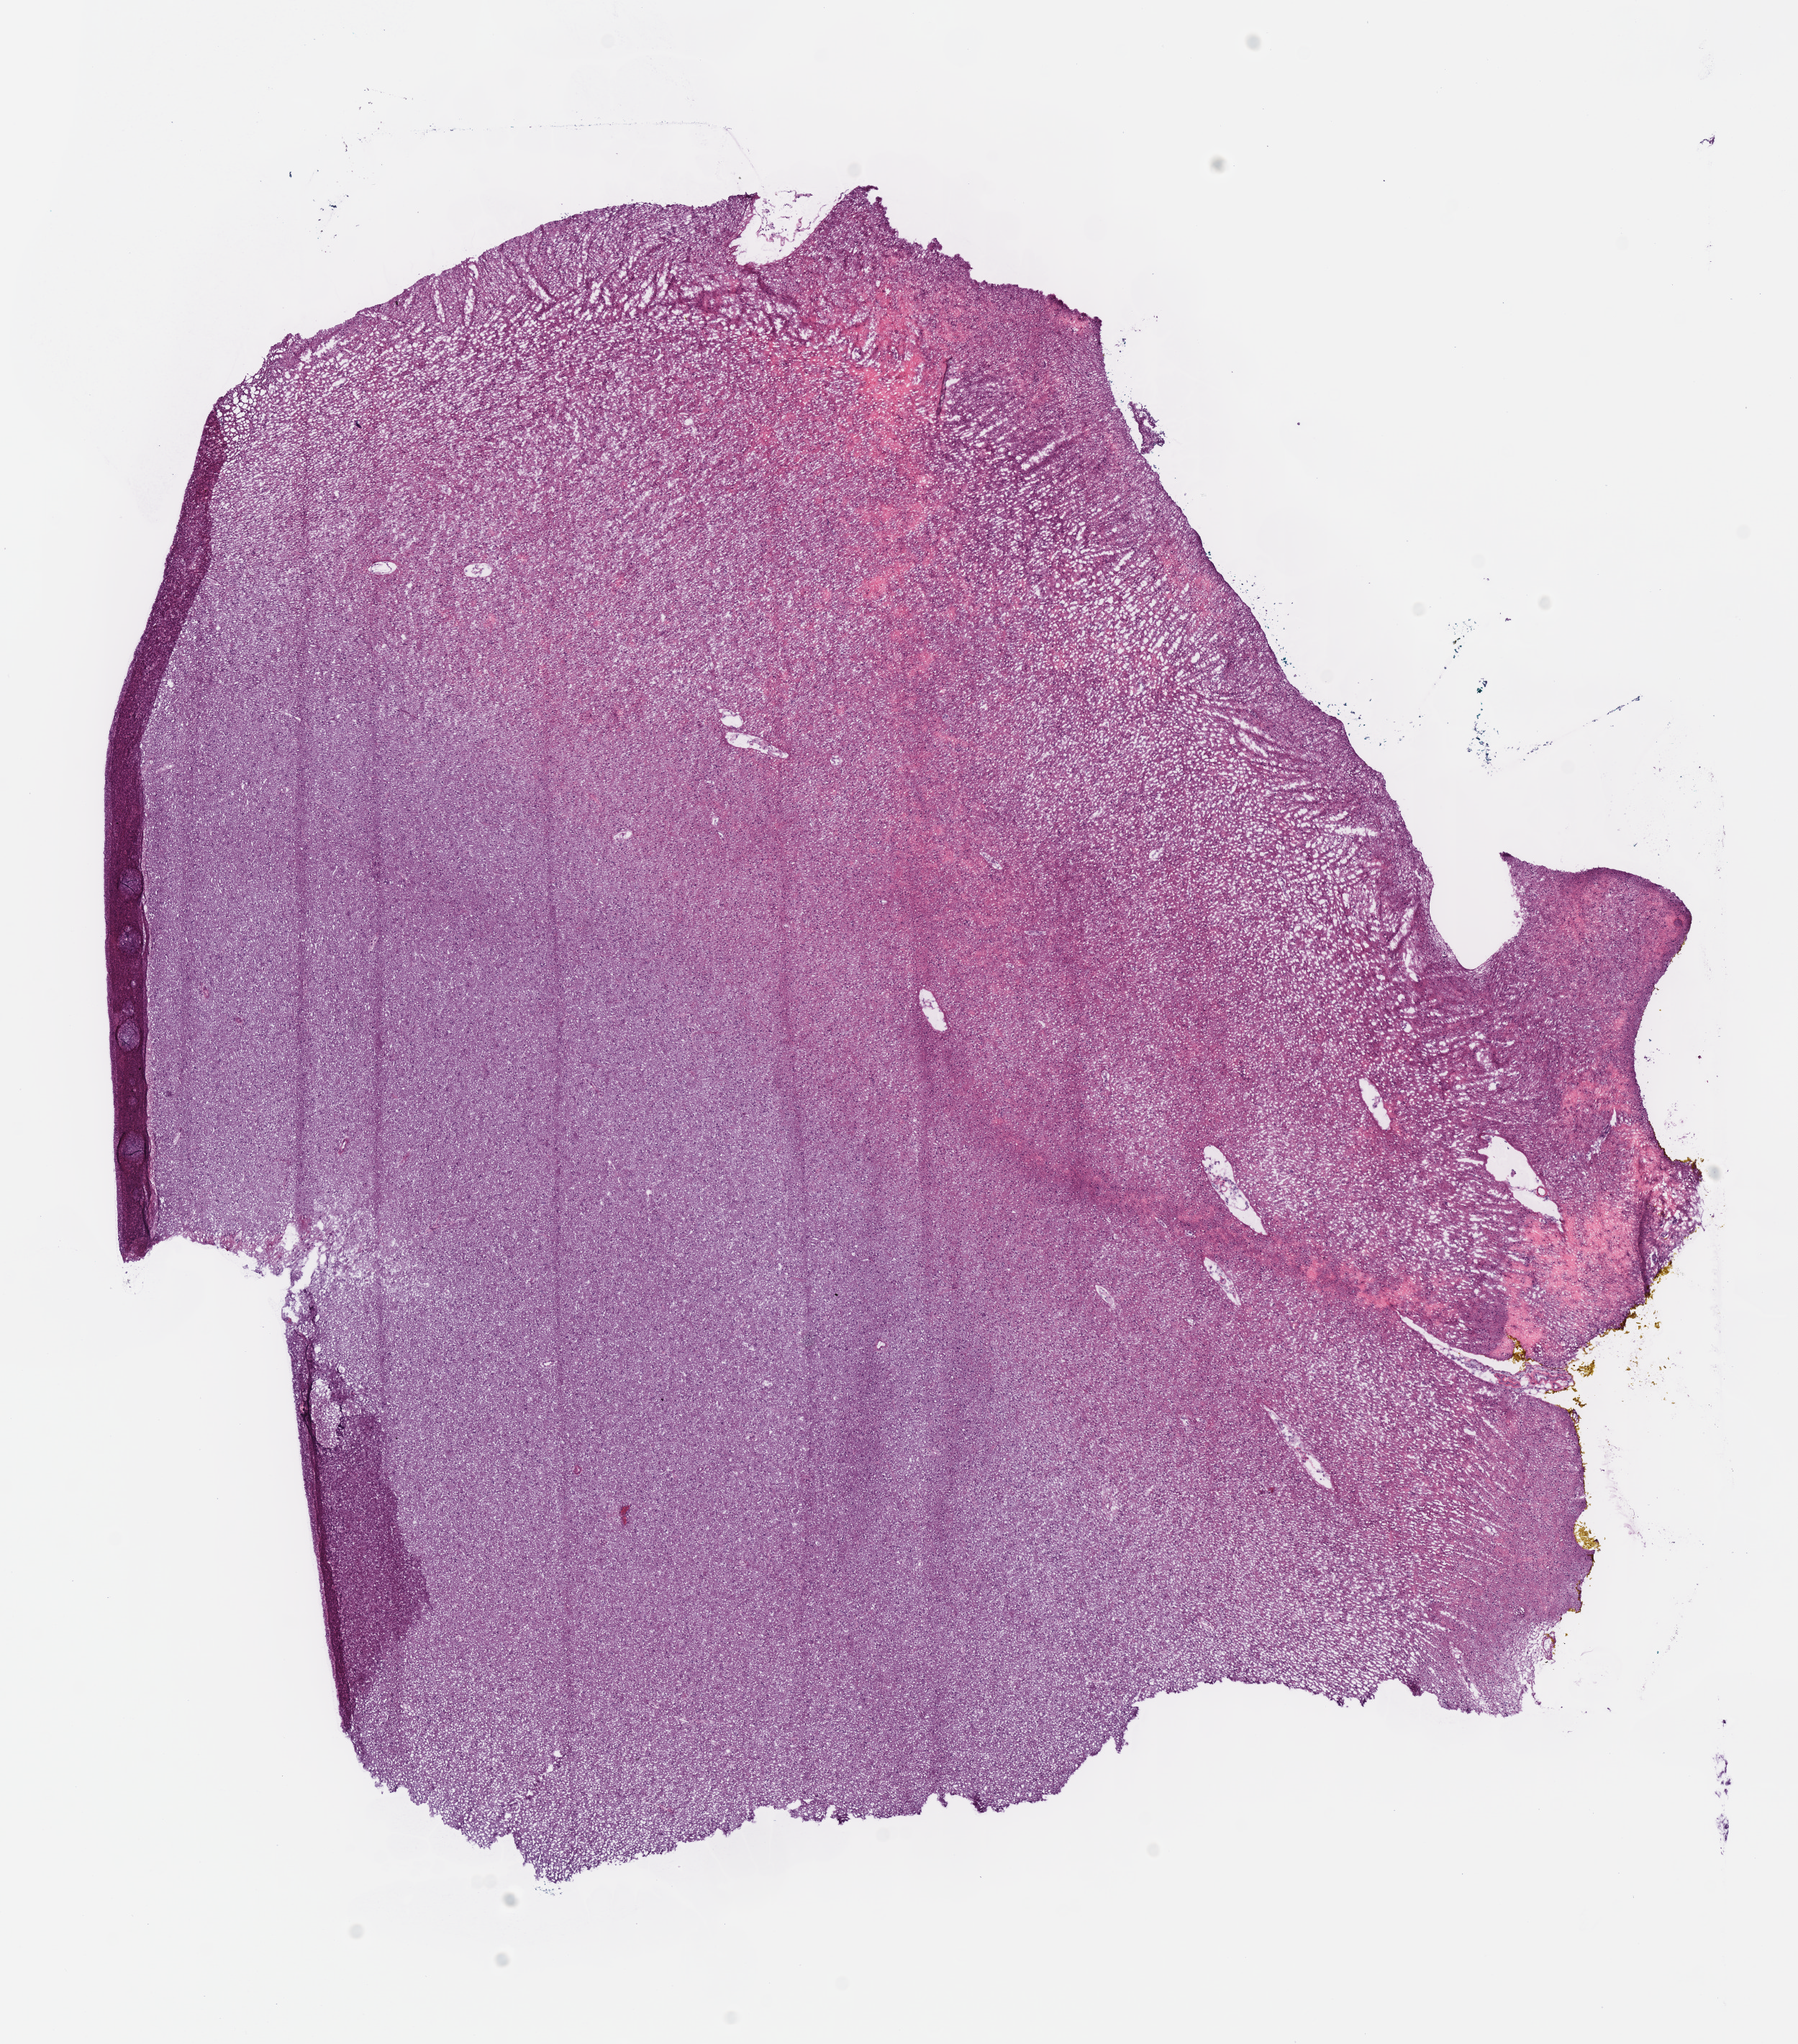
Digitized H&E tissue section (whole slide) — a low-resolution overview of the entire scanned area, about 9.8 x 11.2 mm (acquisition: 40x scan). Frozen section from the bottom of the tissue portion. Primary tumour sample from the brain. Male, age 38 years at initial diagnosis. Histologic grade: G2 (moderately differentiated). Pathologist review of this section (percent, as recorded): tumour cells 100%, tumour nuclei 55%, normal cells 0%, stromal cells 0%, necrosis 0%.
- laterality: right
- pathologic diagnosis: Oligodendroglioma, NOS